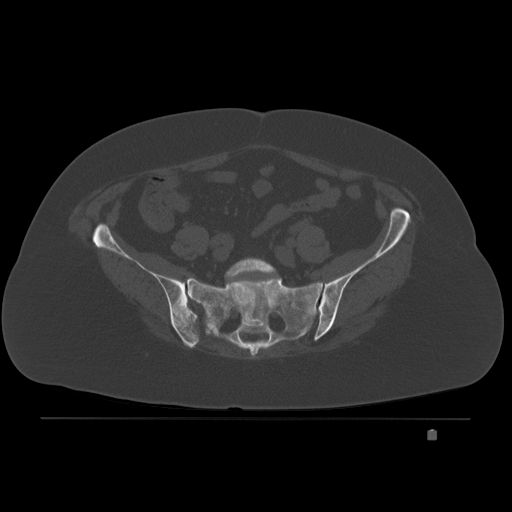
CT including the spine, one axial slice. Slice 22 of 221 in the series (ordered by position). Bone window (W 1800 / L 400 HU). 512 × 512 image matrix, field of view 474 × 474 mm. Patient: female, 63 years. Case-level facts recorded for this patient, not image findings: primary cancer: breast.
Annotated regions visible in this slice (semi-automatic segmentation, software-assisted and operator-edited):
- L5 vertebra: bounding box <224,257,277,280> (left, top, right, bottom; pixels)